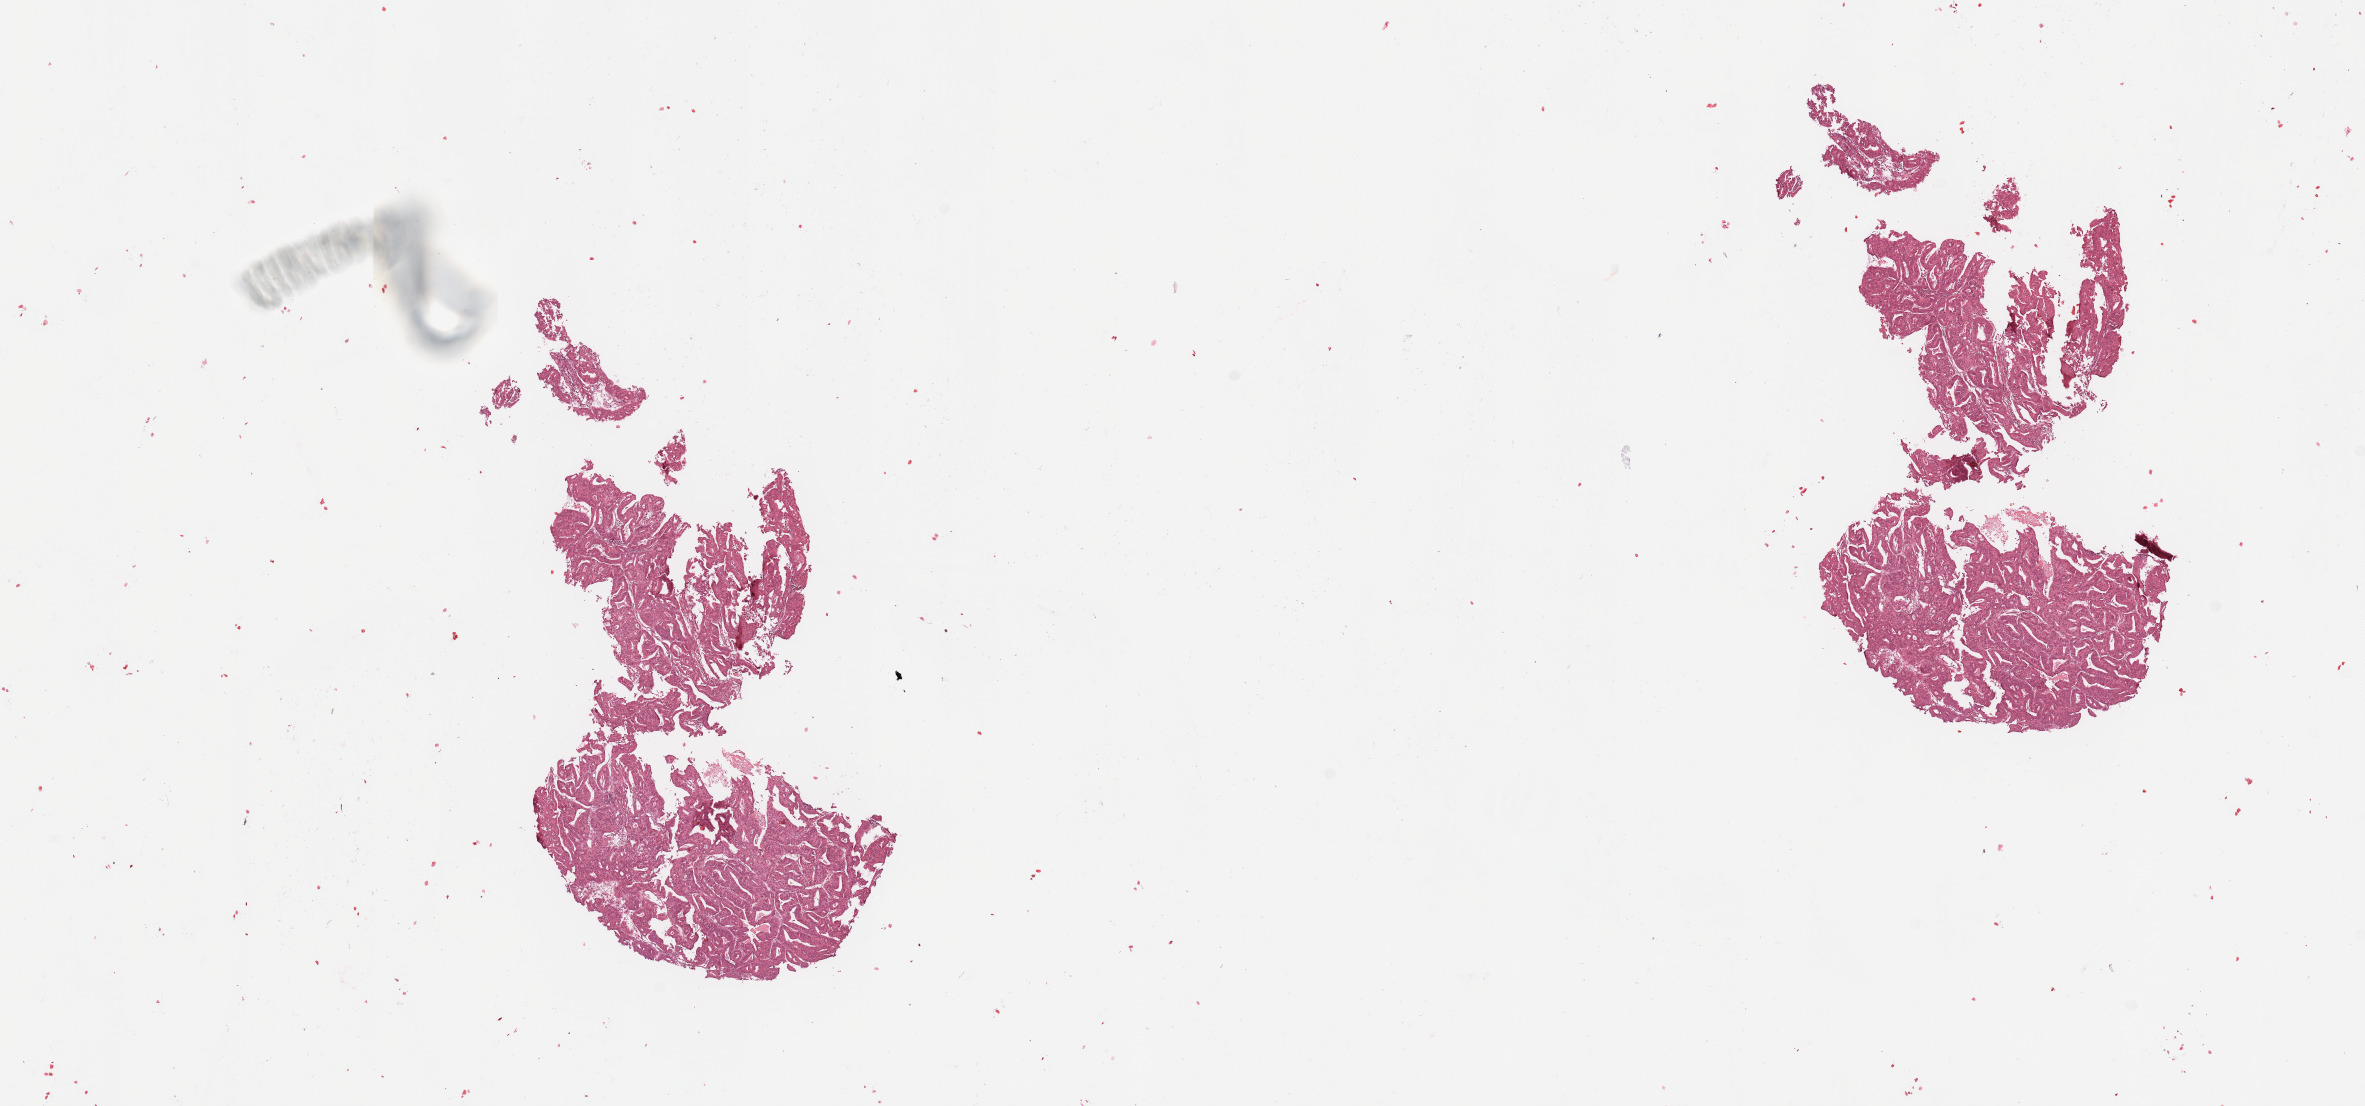
Digitized H&E-stained tissue section (whole slide), a low-resolution overview of the entire scanned area, about 18.7 x 8.7 mm (acquisition: 20x scan). Tumour tissue sample, sampled site: uterus. 61-year-old female patient. Composition of this section per pathologist review: tumour nuclei 90%, necrosis 2%.
Histologic diagnosis: Endometrioid adenocarcinoma, NOS.